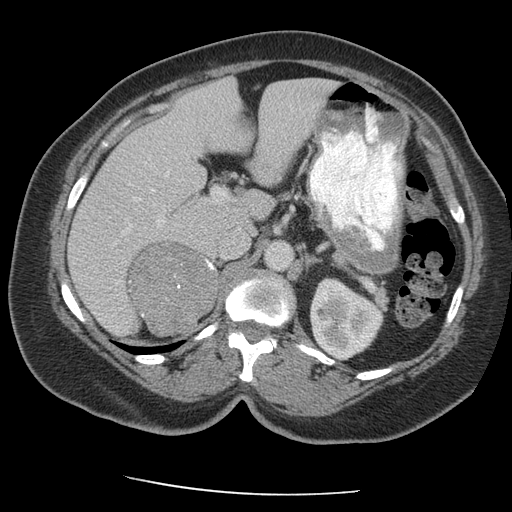
Contrast-enhanced abdominal CT, one axial slice; slice 125 of 163 in the series (ordered by position); reconstruction kernel STANDARD; intravenous contrast given; soft-tissue window (W 400 / L 40 HU); 512 × 512 image matrix. Female patient, age 70 years. Case-level facts recorded for this patient, not image findings: diagnosis: adrenocortical carcinoma; tumour side: right adrenal; tumour size at pathology: 9.5 cm; Ki-67 index: 5 %; stage (as recorded): 2.
Annotated regions visible in this slice (semi-automatically segmented with operator editing):
- mass: bounding box <130,243,214,334> (left, top, right, bottom; pixels)